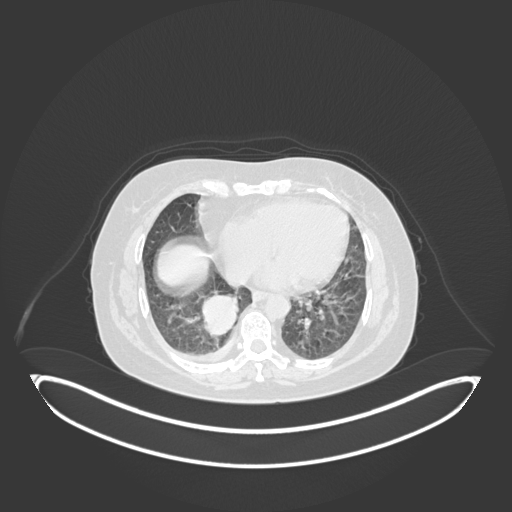
Chest CT, one axial slice. Slice 51 of 231 in the series (ordered by position). Reconstruction kernel B30f. Lung window (W 1500 / L -600 HU). 1 mm slice thickness. 512 × 512 image matrix, field of view 500 × 500 mm. Patient: female, 56 years. From the clinical record (not read from this slice): clinical TNM (as recorded): T2b N1 M0.
Outlined on this slice (rectangle marked by the reading radiologist):
- lung tumour (recorded histology: small cell carcinoma): bounding box [x1, y1, x2, y2] px = [203, 293, 244, 336]